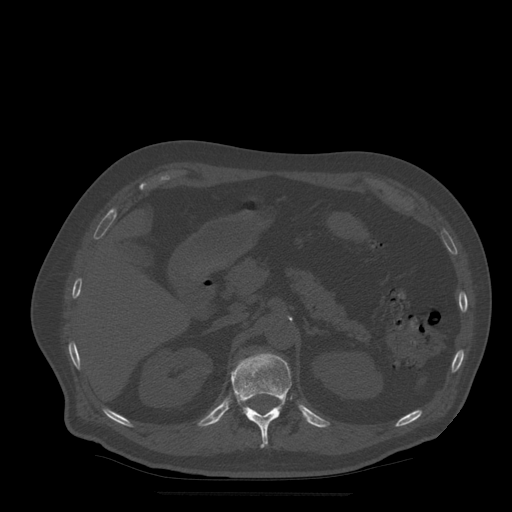
CT including the spine, one axial slice; position 216 of 522 along the scan axis; bone window (W 1800 / L 400 HU); 512 × 512 image matrix, field of view 420 × 420 mm. Patient age 72 years. Case-level facts recorded for this patient, not image findings: primary cancer: prostate.
Annotated regions visible in this slice (semi-automatically segmented with operator editing):
- T12 vertebra: bounding box (x1, y1, x2, y2) in pixels: (231, 353, 292, 448)